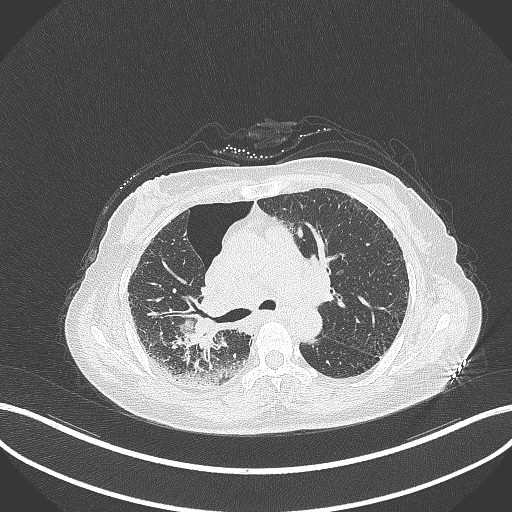
Chest CT, one axial slice. 120 kVp. Lung window (W 1500 / L -600 HU). 1 mm slice thickness. 512 × 512 image matrix, field of view 400 × 400 mm. Female patient, age 64 years. From the clinical record (not read from this slice): clinical TNM (as recorded): T3 N3 M0.
Structures marked on this image (rectangle marked by the reading radiologist):
- lung tumour (recorded histology: squamous cell carcinoma): bounding box <175,310,226,353> (left, top, right, bottom; pixels)